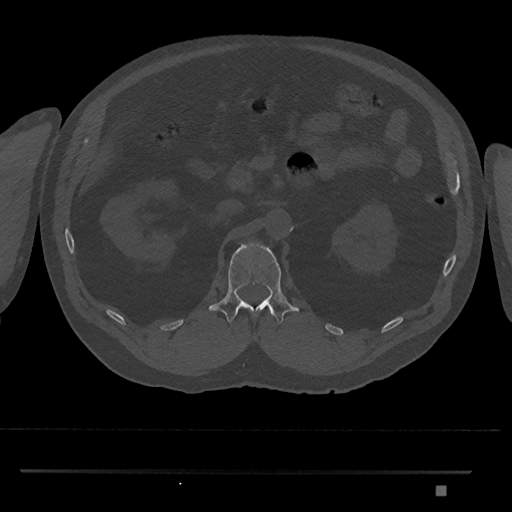
CT including the spine, one axial slice. Position 829 of 1134 along the scan axis. Reconstruction kernel Br40s/3. Bone window (W 1800 / L 400 HU). 0.5 mm slice thickness. 512 × 512 image matrix. Male patient, age 65 years. From the clinical record (not read from this slice): primary cancer: prostate.
Outlined on this slice (semi-automatically segmented with operator editing):
- L1 vertebra: bounding box (x1, y1, x2, y2) in pixels: (209, 242, 300, 324)
- T12 vertebra: (270, 312, 272, 314)